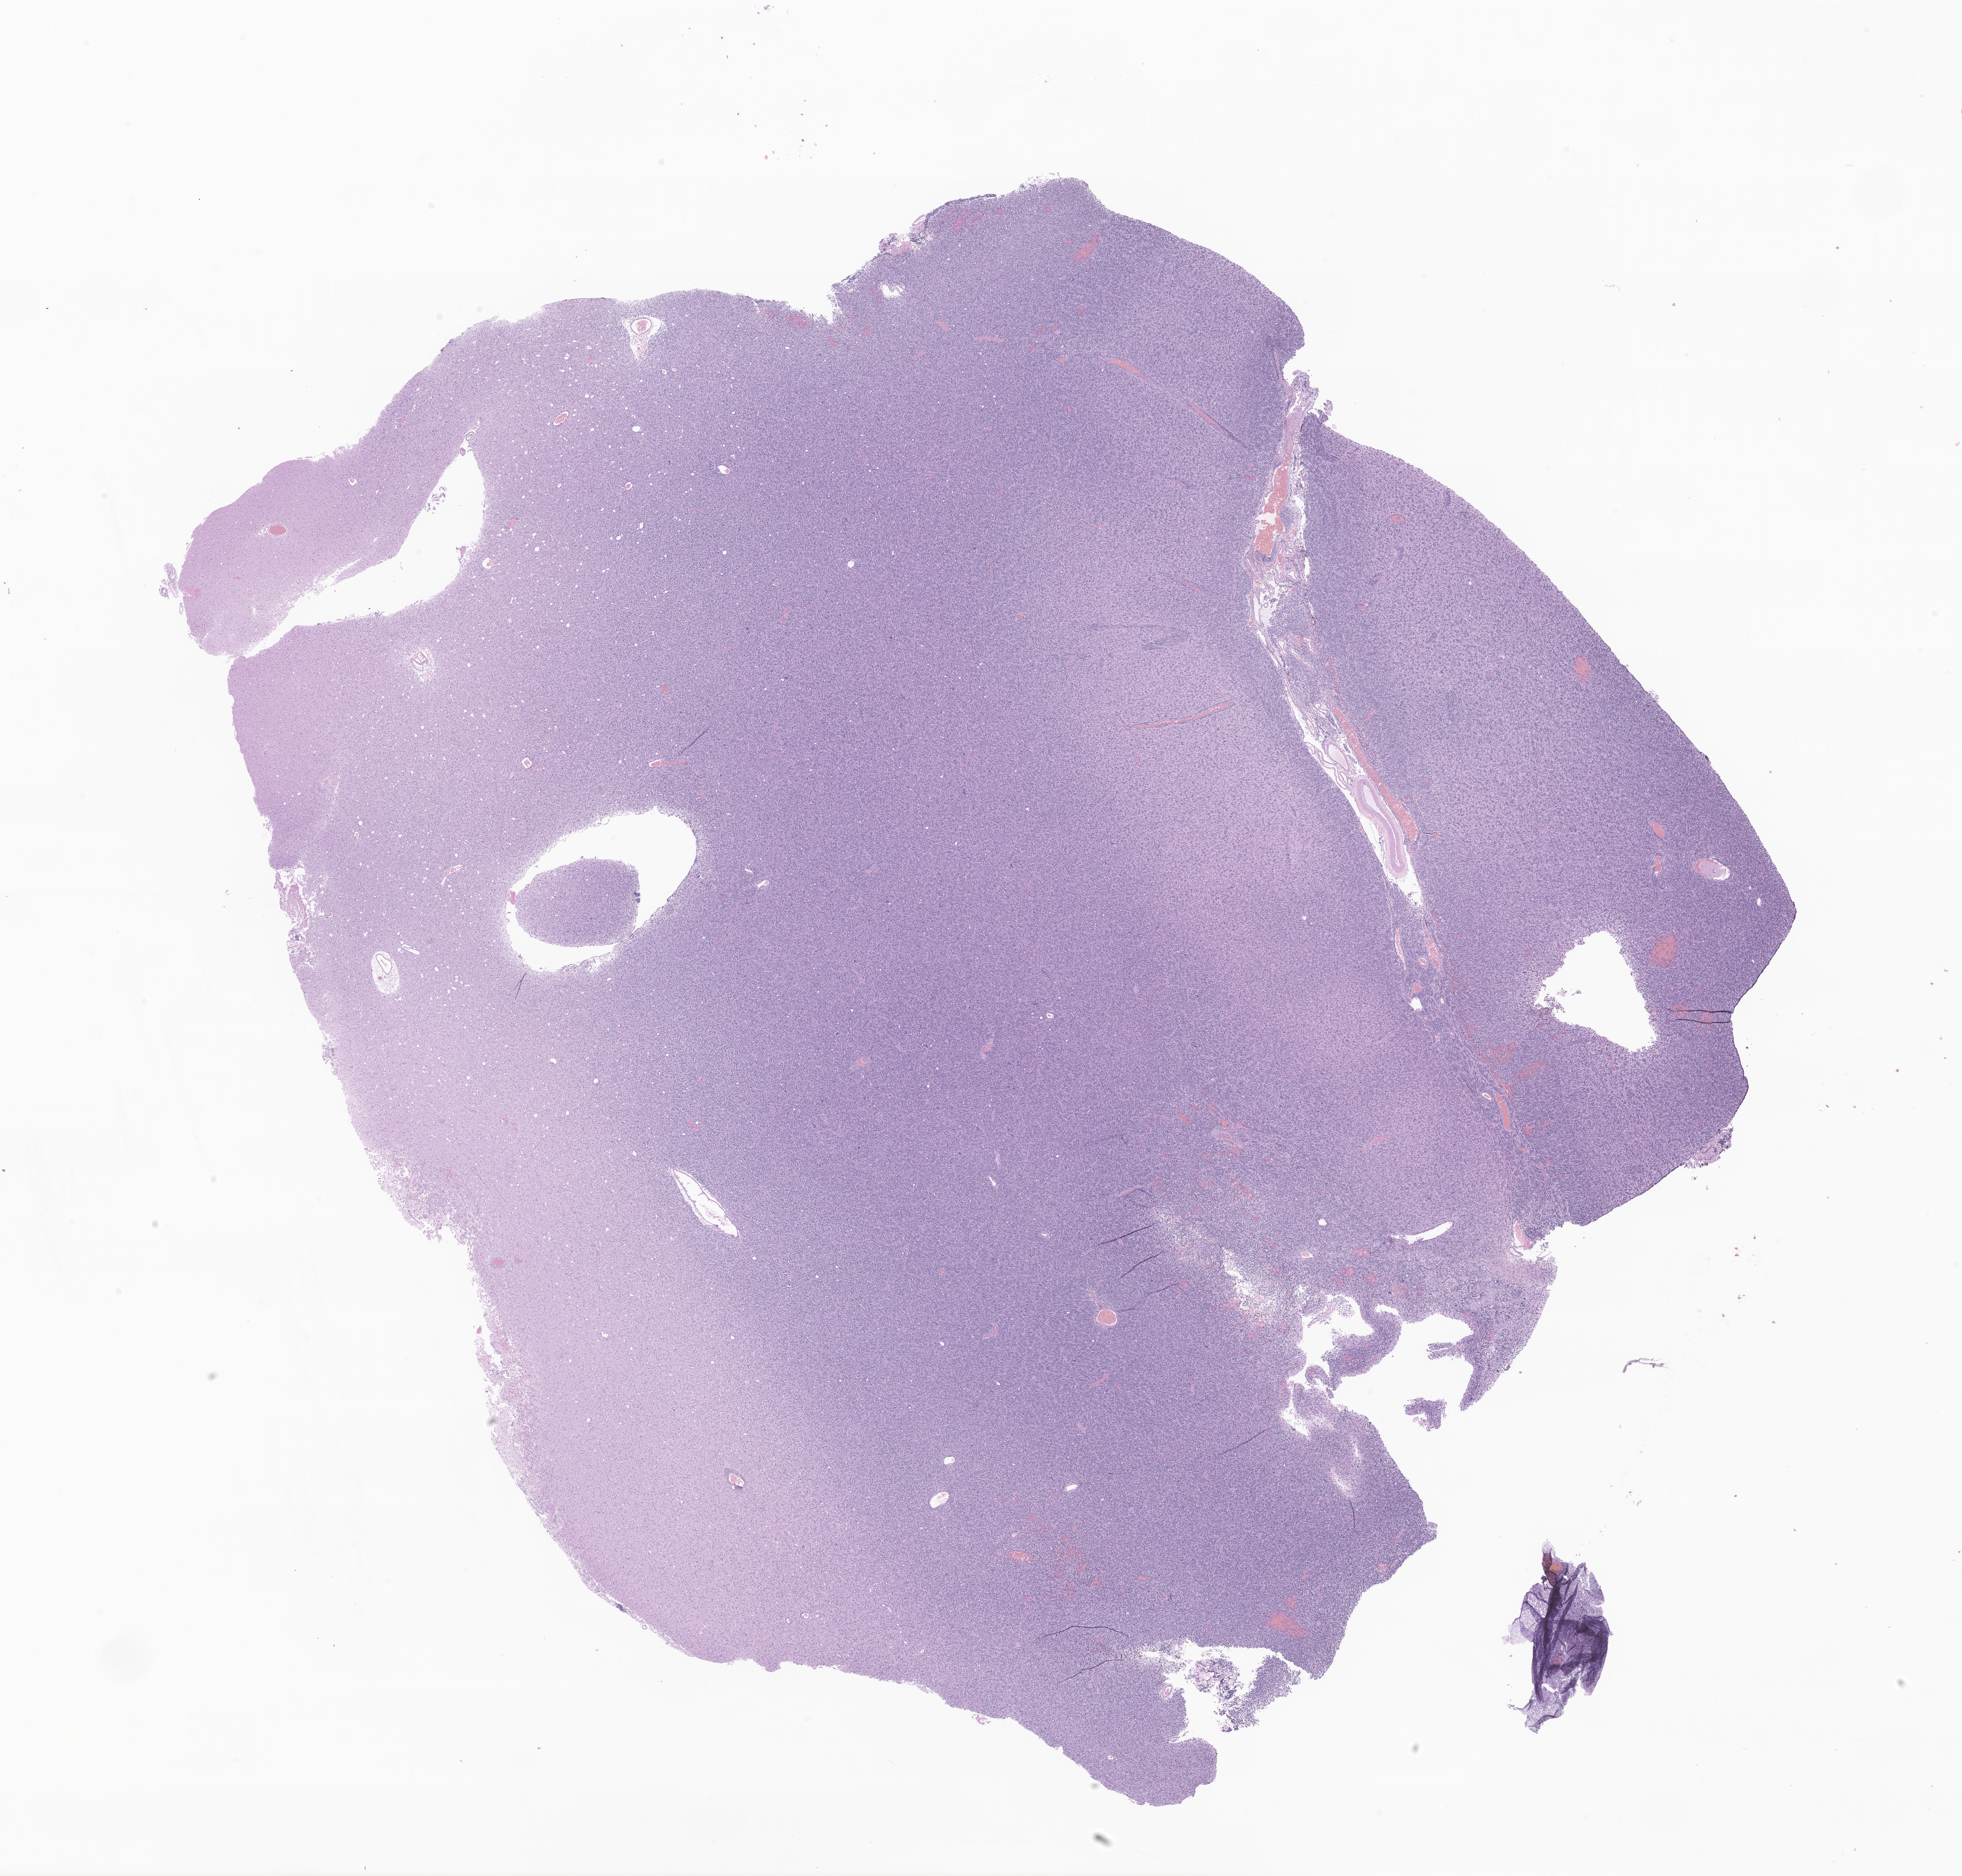
Digitized haematoxylin and eosin-stained section of tumor tissue from the parietal lobe, whole scanned area (about 22.2 x 21.2 mm) shown as a low-resolution overview. Formalin-fixed paraffin-embedded section. Patient male; age 194 months (16 years 2 months).
Diagnosis: Glioma, malignant.